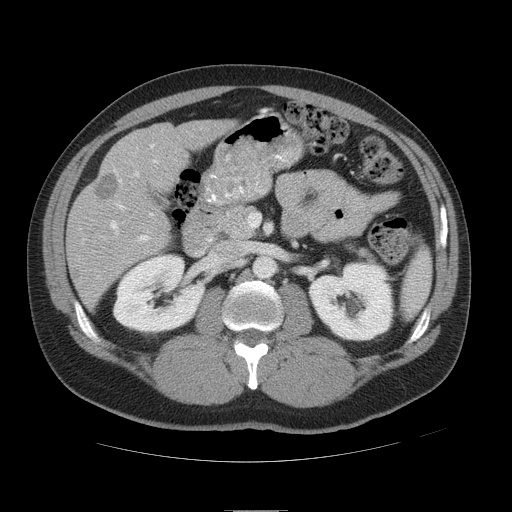
Contrast-enhanced abdominal CT, one axial slice. Slice 23 of 49 in the series (ordered by position). Intravenous contrast given. Soft-tissue window (W 400 / L 40 HU). 5 mm slice thickness. 512 × 512 image matrix, field of view 425 × 425 mm. Male patient, age 52 years. From the clinical record (not read from this slice): diagnosis: colorectal cancer liver metastases, imaged before liver resection; multiple liver metastases: yes; largest metastasis: 5.1 cm; disease in both lobes: yes.
Annotated regions visible in this slice (outlined manually by an expert reader):
- hepatic veins: bounding box (x1, y1, x2, y2) in pixels: (110, 143, 155, 234)
- liver: (69, 120, 230, 304)
- planned liver remnant (the part of the liver to remain after resection): (133, 120, 231, 178)
- portal vein (with intrahepatic branches): (113, 165, 154, 243)
- liver metastasis: (93, 175, 120, 202)